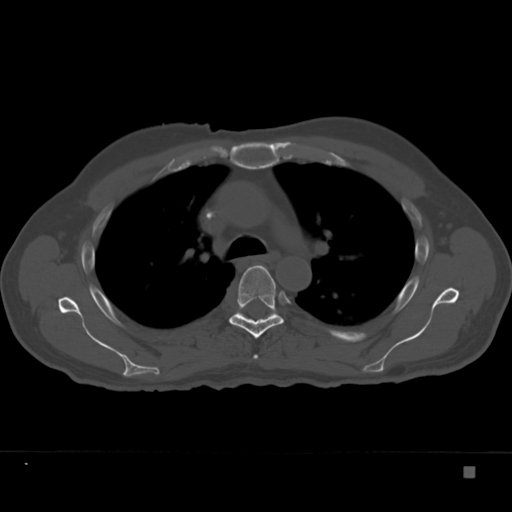
CT including the spine, one axial slice; slice 257 of 332 in the series (ordered by position); reconstruction kernel Br40s; 120 kVp; bone window (W 1800 / L 400 HU); 1.5 mm slice thickness; 512 × 512 image matrix. Male patient, age 72 years. Case-level facts recorded for this patient, not image findings: primary cancer: skeletal.
Structures marked on this image (semi-automatically segmented with operator editing):
- T4 vertebra: bounding box [x1, y1, x2, y2] px = [253, 355, 258, 359]
- T5 vertebra: [229, 265, 284, 339]
- T6 vertebra: [237, 311, 274, 318]